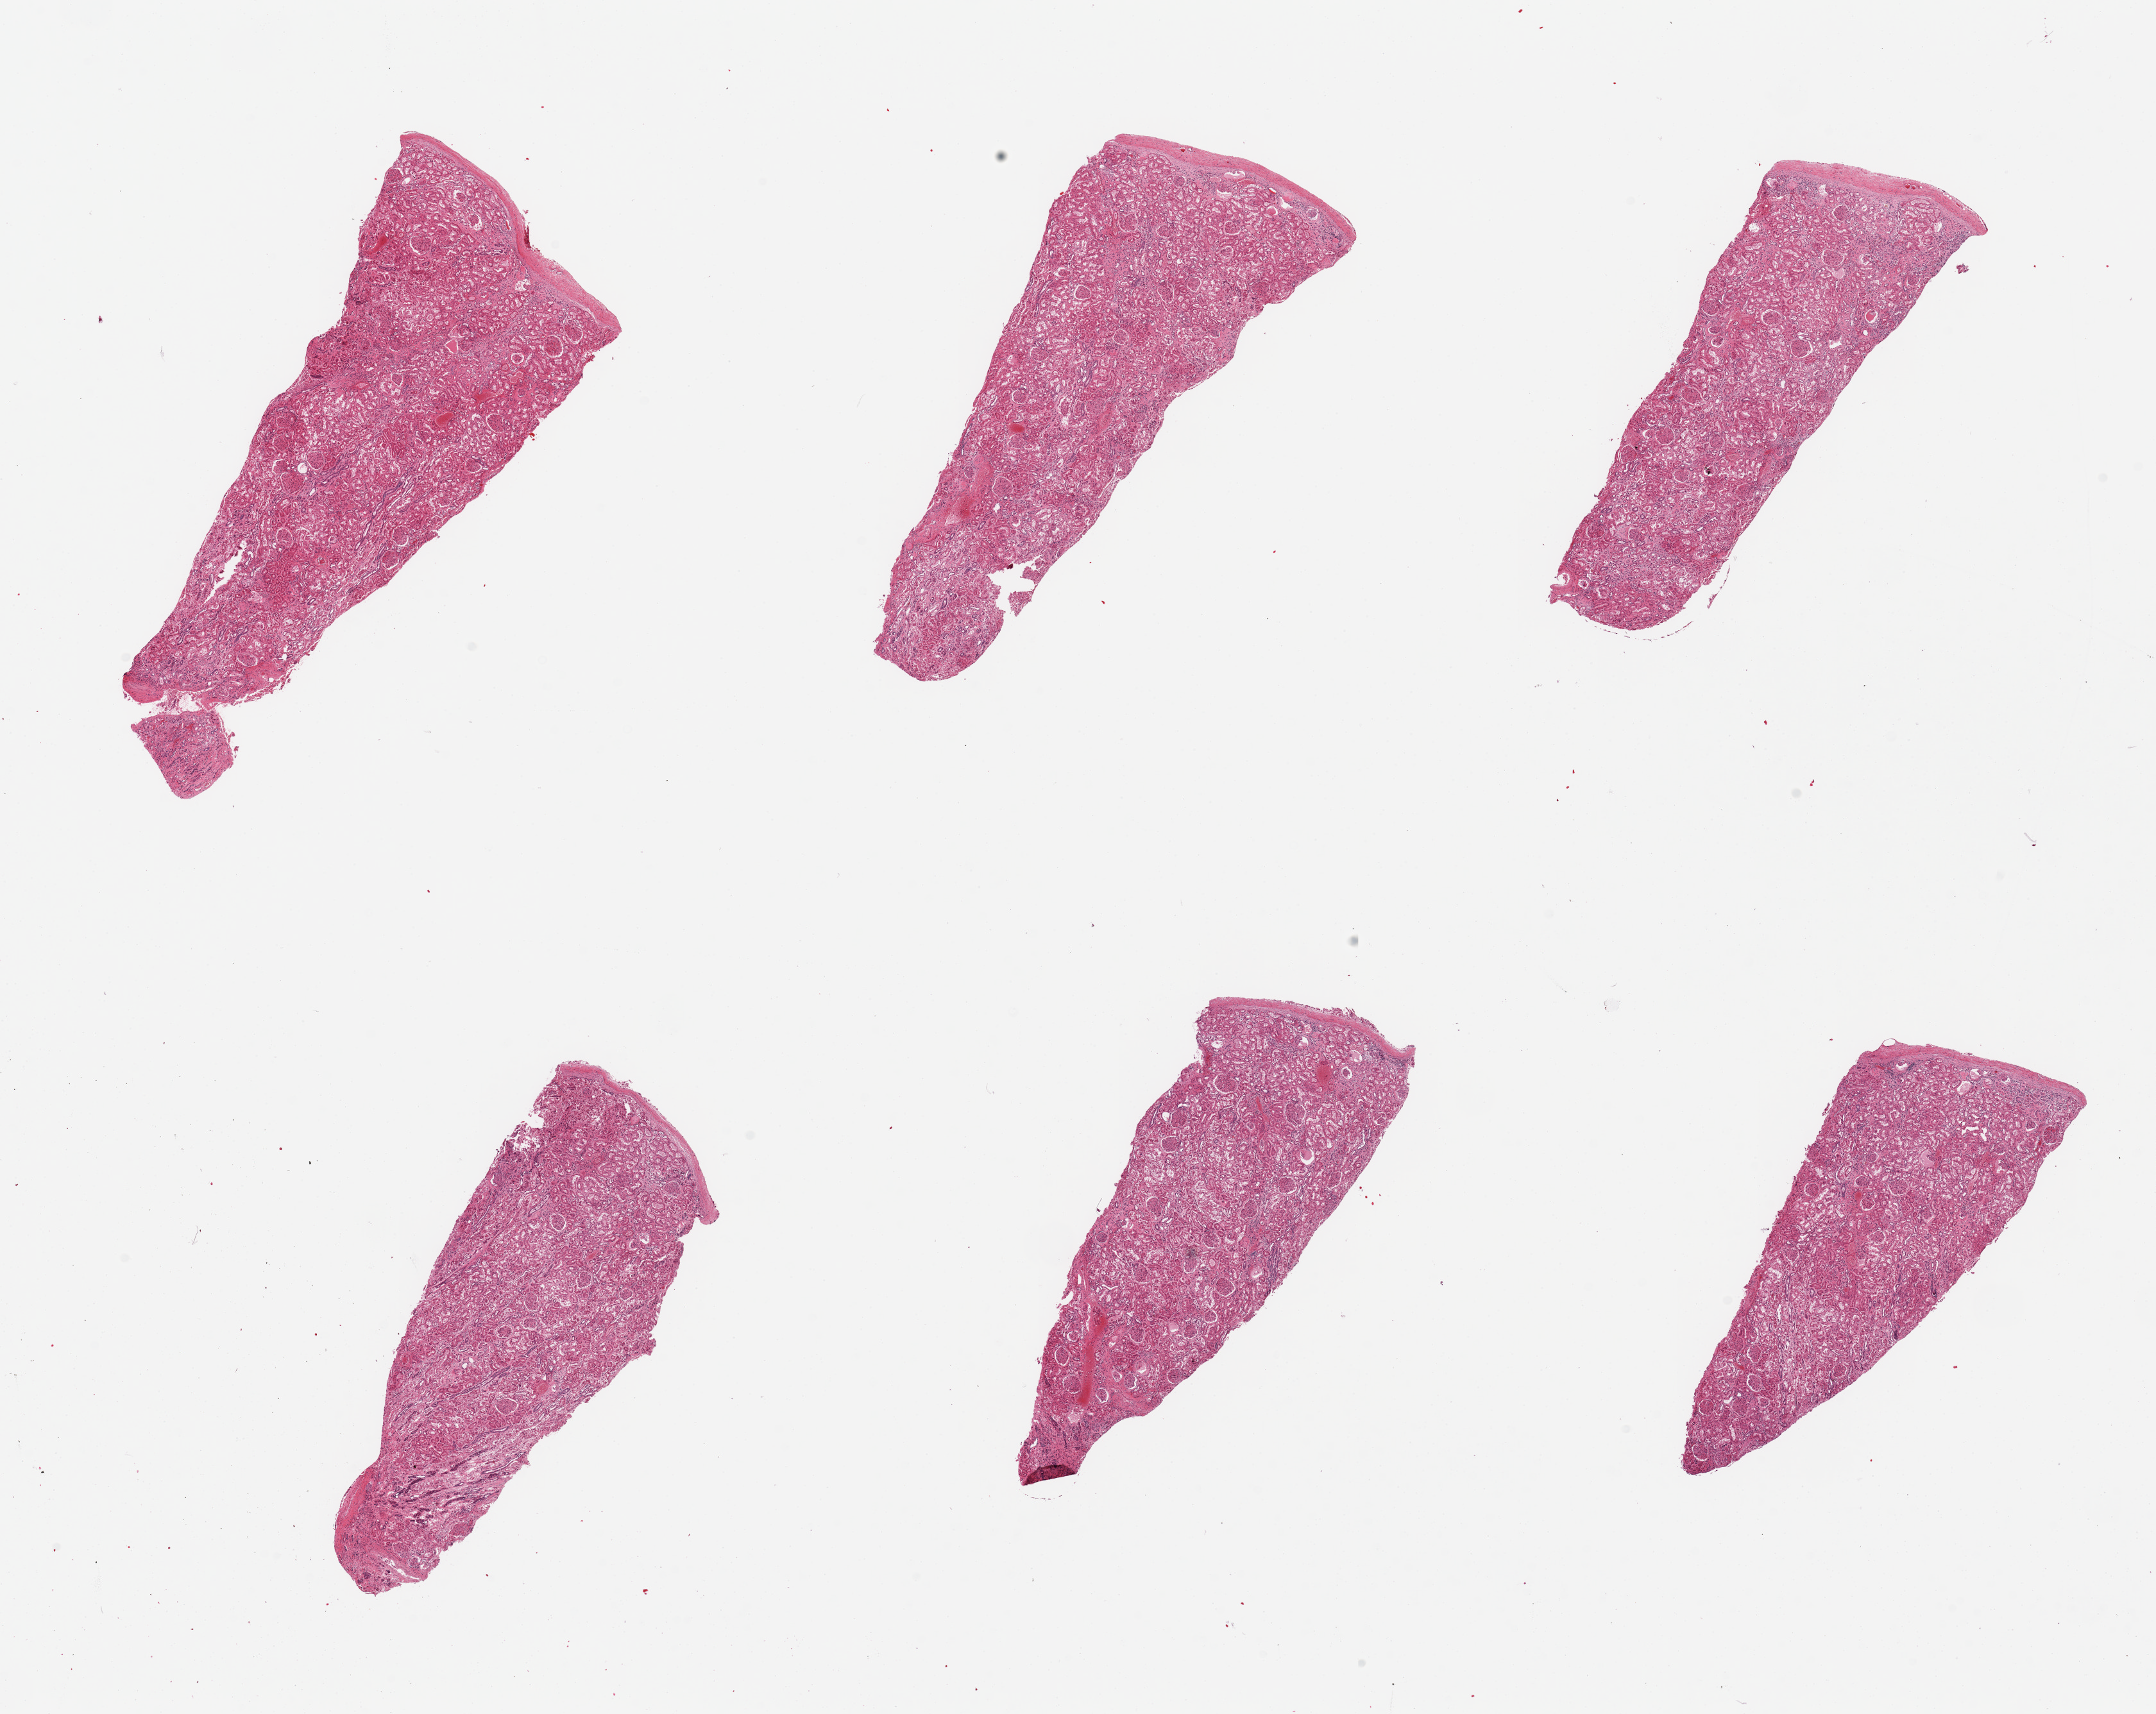
Whole-slide image, hematoxylin and eosin (H&E) stain, brightfield, low-resolution overview of the scanned area, about 26.6 x 21.1 mm (acquisition: 20x scan). PAXgene-fixed paraffin-embedded (PFPE) section. Sampled site (target tissue): renal cortex. Tissue donor sample. Female donor.
Reviewer comment on this tissue sample: 6 pieces, glomeruli present, moderately-markedly autolyzed.